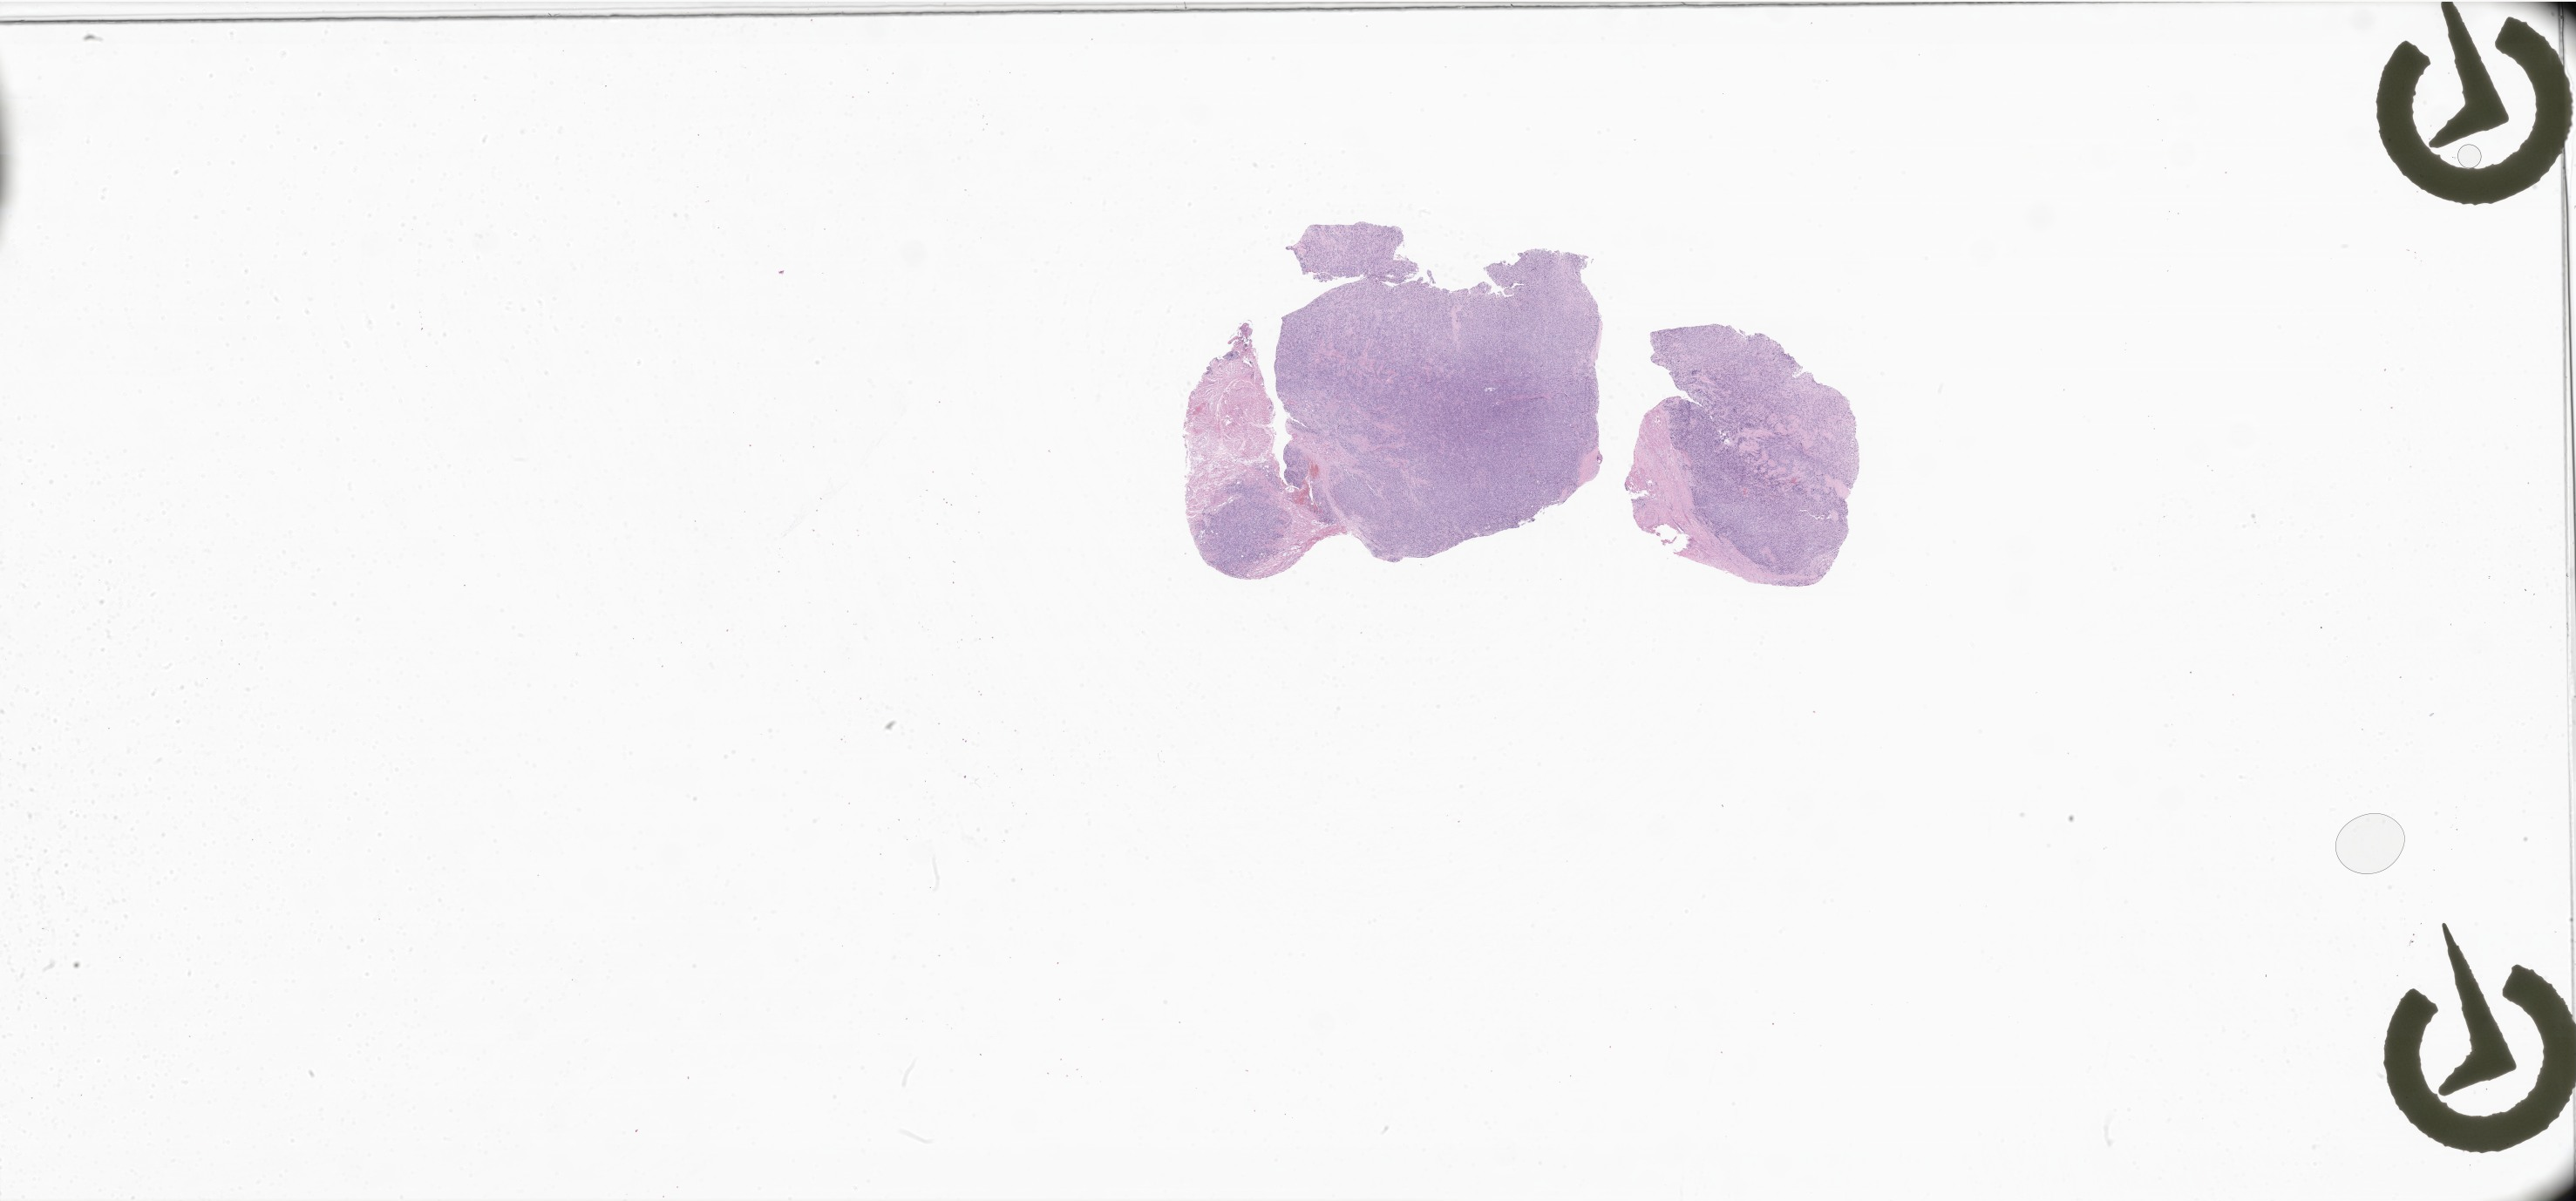
Whole-slide image, H&E stain of tumor tissue from the mandible — a low-resolution overview of the entire scanned area, about 49.8 x 23.2 mm; FFPE section. Male patient, age 34 months.
* diagnosis (ICD-O-3 morphology term): Embryonal rhabdomyosarcoma, NOS